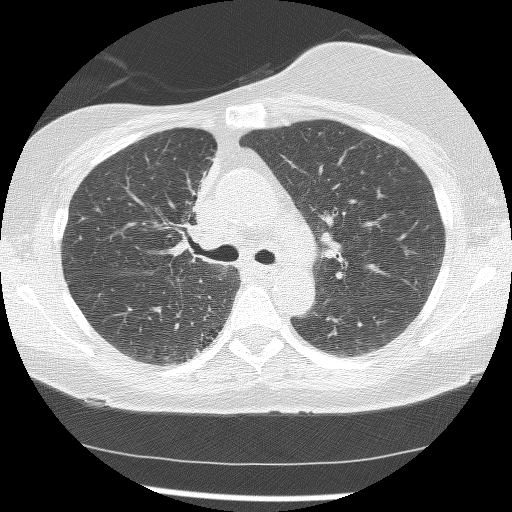
Low-dose screening chest CT, axial slice; first (baseline) screen; lung window (W 1500 / L -600 HU); 2.5 mm slice thickness; lung (sharp) reconstruction kernel (BONE); slice 55 of 172 in the series. Female, age 56 years at enrolment. Current smoker at enrolment.
Lesion marked by an expert reader, bounding box <162,159,218,262> (left, top, right, bottom; pixels). The screening reader recorded 2 non-calcified nodules or masses ≥4 mm on this exam; which of them this box marks is not recorded. Official screen result: positive, change unspecified: nodule(s) >= 4 mm or enlarging nodule(s), mass(es), or other non-specific abnormalities suspicious for lung cancer. Lung cancer was diagnosed 1185 days after this screen: adenocarcinoma, NOS, right upper lobe, stage IIIB (AJCC 6th edition), 8 mm at pathology.